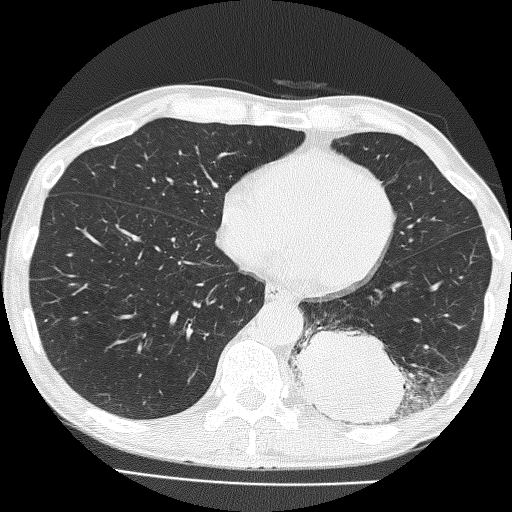
Chest CT (low-dose screening protocol), one axial image, baseline screening round, lung window (W 1500 / L -600 HU), slice 102 of 160 in the series. Male, age 58 years at enrolment. Current smoker at enrolment.
• Lesion marked by an expert reader, bounding box (x1, y1, x2, y2) in pixels: (294, 300, 427, 435).
• The screening reader recorded 2 non-calcified nodules or masses ≥4 mm on this exam (left lower lobe, left upper lobe); which of them this box marks is not recorded.
• Official screen result: positive, change unspecified: nodule(s) >= 4 mm or enlarging nodule(s), mass(es), or other non-specific abnormalities suspicious for lung cancer.
• Lung cancer was diagnosed 39 days after this screen: non-small cell carcinoma, left lower lobe, poorly differentiated (G3), stage IV (AJCC 6th edition), 74 mm at pathology.